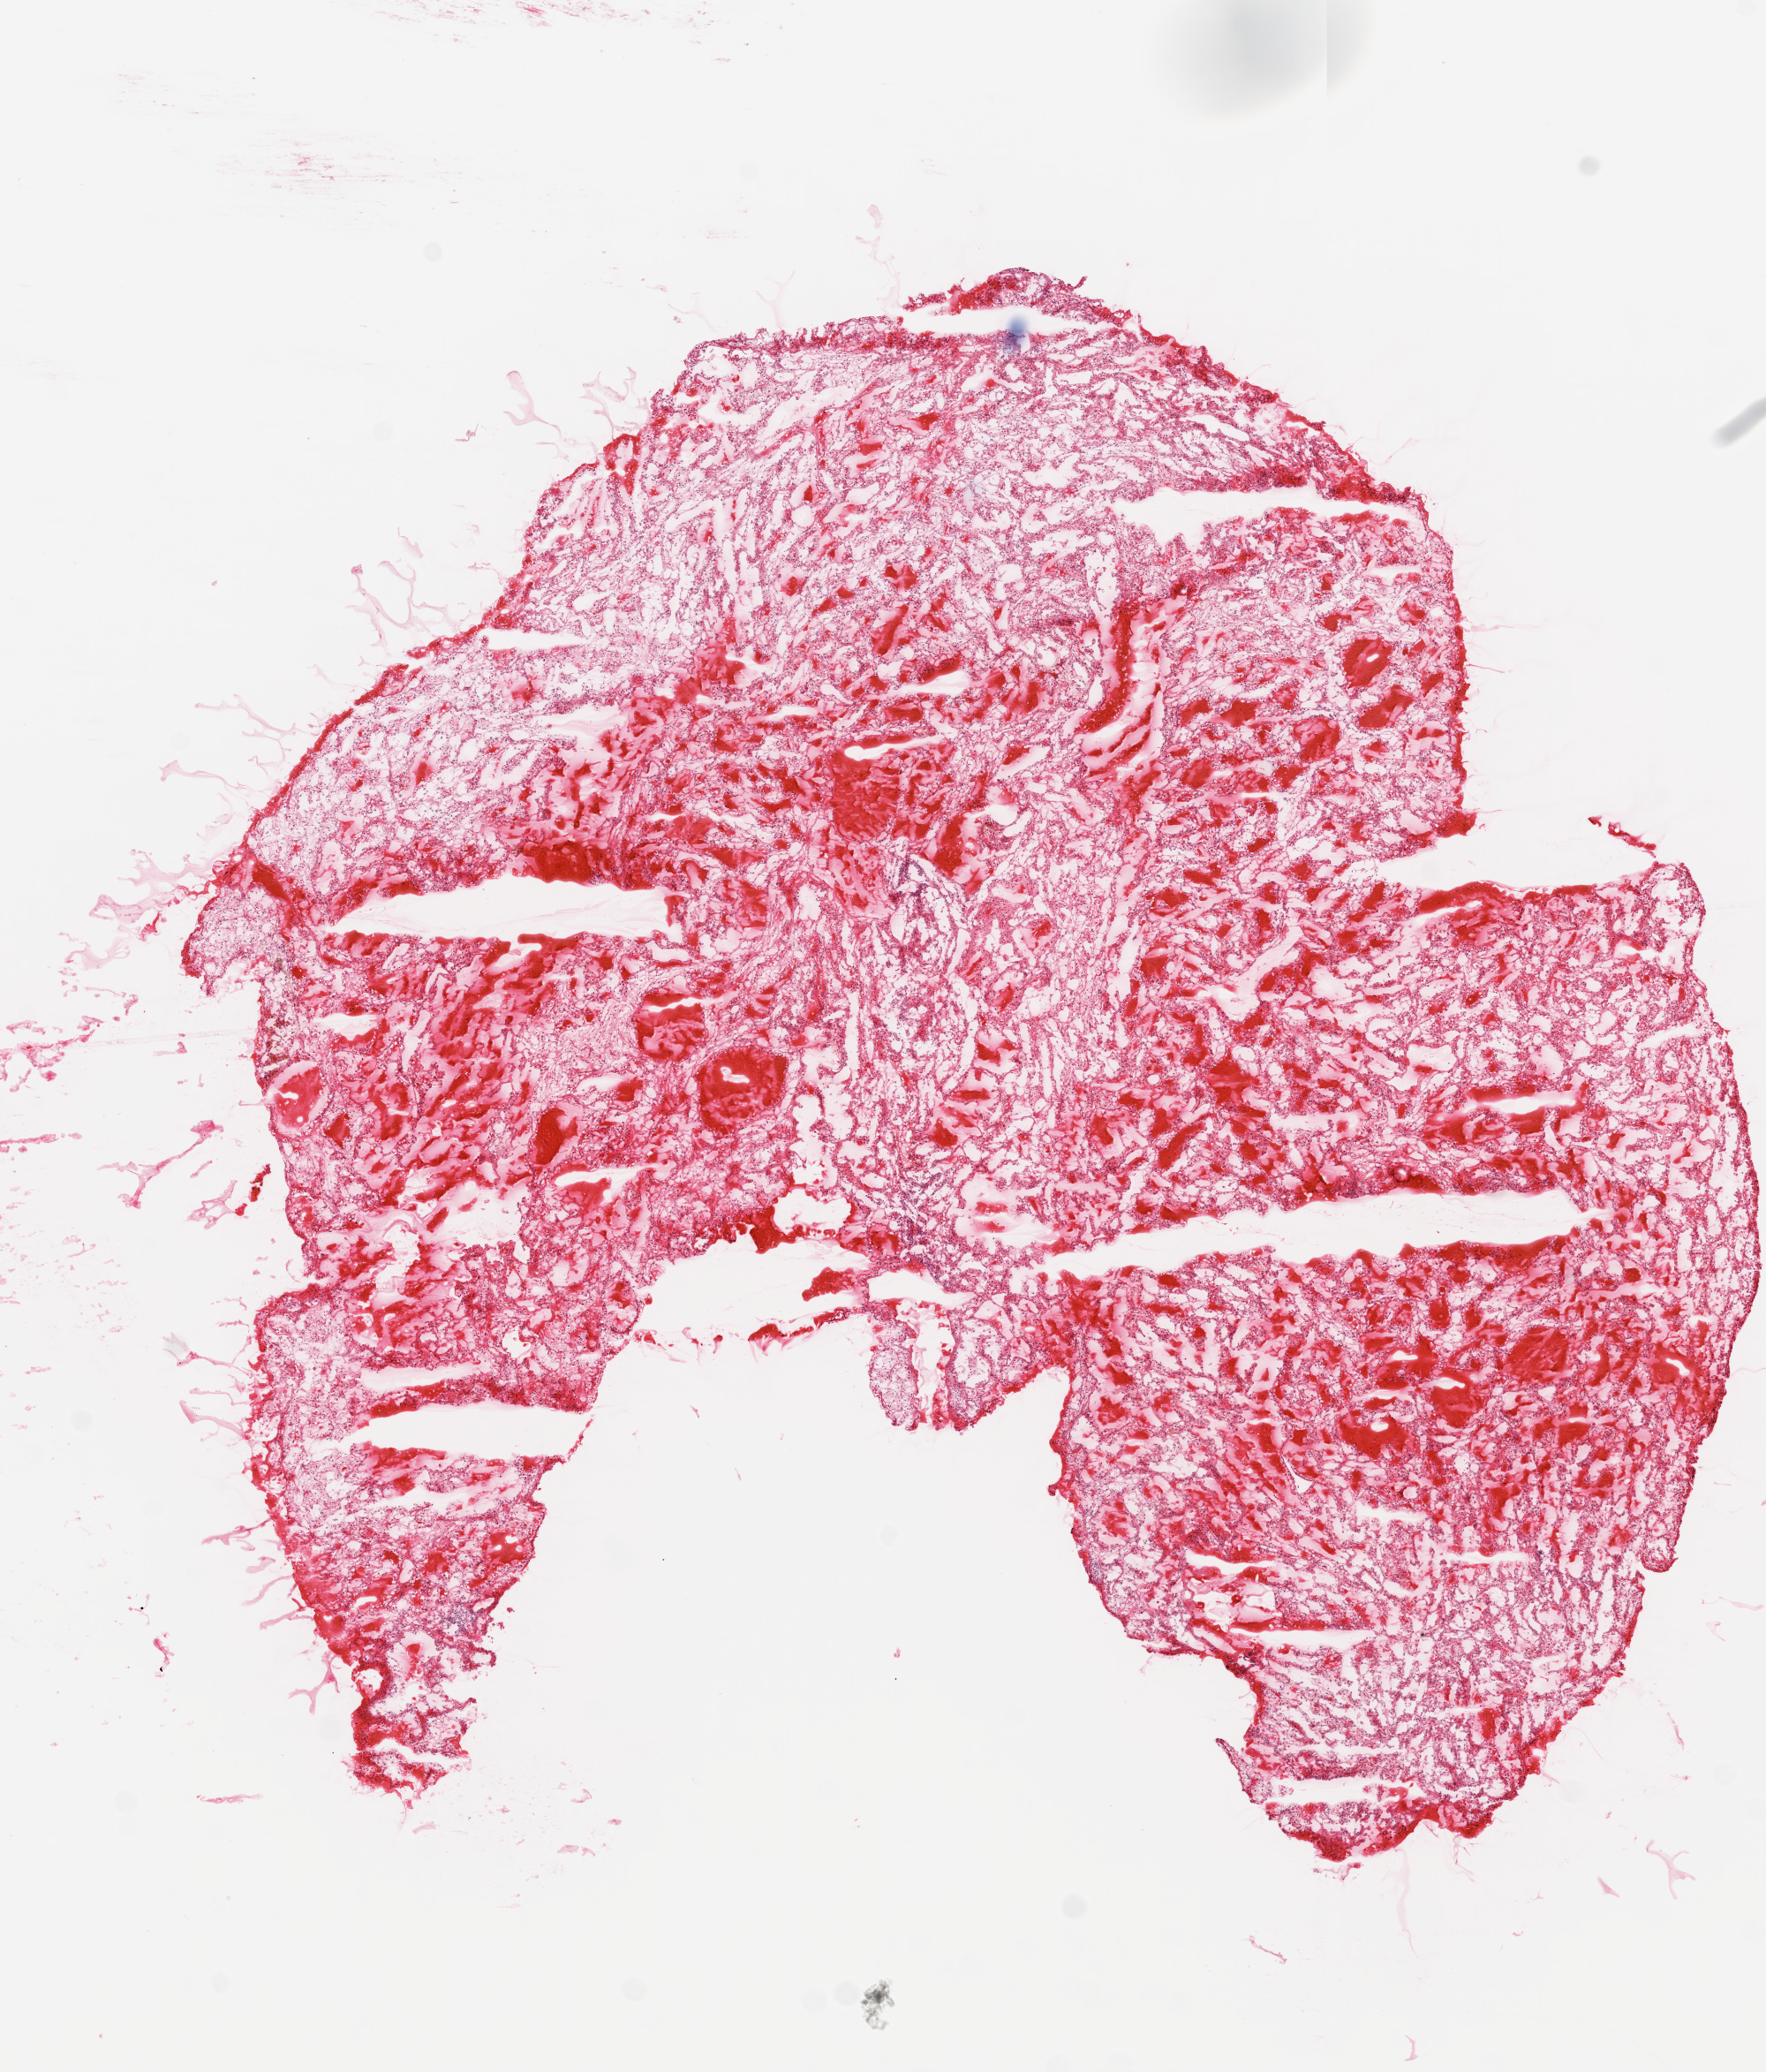
H&E-stained whole-slide image — a low-resolution overview of the entire scanned area, about 8.0 x 9.4 mm (acquisition: 20x scan), frozen section, primary tumour sample from the kidney. Male, age 63 years at initial diagnosis. Histologic grade: G3 (poorly differentiated). Pathologist review of this section (percent, as recorded): tumour cells 95%, tumour nuclei 90%, normal cells 0%, stromal cells 5%, necrosis 0%.
Diagnosis: Clear cell adenocarcinoma, NOS. AJCC pathologic stage: III. Laterality: right.